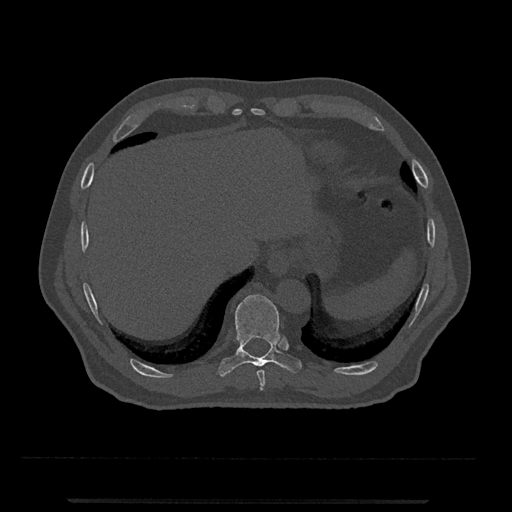
CT including the spine, one axial slice. Position 528 of 797 along the scan axis. 120 kVp. Bone window (W 1800 / L 400 HU). 0.5 mm slice thickness. 512 × 512 image matrix, field of view 419 × 419 mm. Patient: male, 63 years. From the clinical record (not read from this slice): primary cancer: prostate.
Annotated regions visible in this slice (semi-automatic segmentation, software-assisted and operator-edited):
- T10 vertebra: box from (x=218, y=295) to (x=302, y=377) px
- T9 vertebra: (x=257, y=370)–(x=265, y=391)